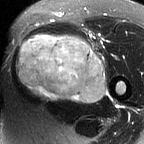
MRI of an extremity soft-tissue mass, one axial slice; position 36 of 60 along the scan axis; T2-weighted fat-saturated; MR volume resampled by the dataset authors to the PET/CT grid (not the native acquisition matrix); 3.27 mm slice thickness; 144 × 144 image matrix, field of view 141 × 141 mm. Female patient. From the clinical record (not read from this slice): histological type: pleiomorphic leiomyosarcoma; grade: intermediate; site of the primary tumour: left thigh.
Structures marked on this image (expert contour drawn on MRI and transferred to this co-registered scan by the dataset authors):
- gross tumour volume including surrounding oedema: bounding box [x1, y1, x2, y2] px = [16, 35, 105, 103]
- gross tumour volume (mass): [16, 35, 105, 102]